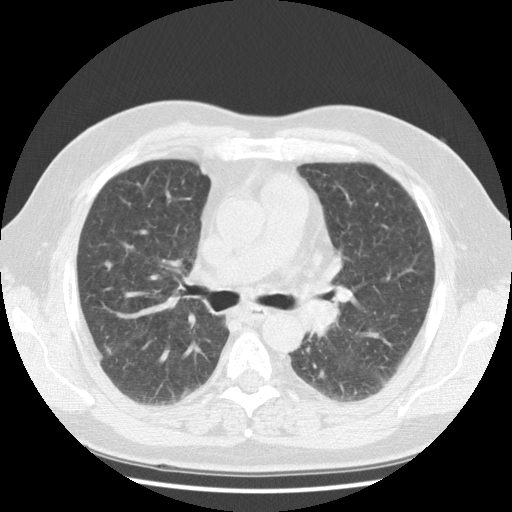
Low-dose screening chest CT, one axial slice. Slice 68 of 108 in the series (ordered by position). Reconstruction kernel STANDARD. Lung window (W 1500 / L -600 HU). 2.5 mm slice thickness. 512 × 512 image matrix, field of view 350 × 350 mm.
Structures marked on this image (expert manual segmentation):
- lesion 1 (tumor, hilum of left lung): bounding box [x1, y1, x2, y2] px = [297, 298, 338, 333]